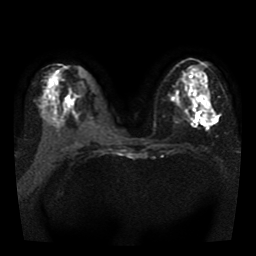
Breast MRI, one axial slice. Slice 17 of 41 in the series (ordered by position). Diffusion-weighted series; image 2 of 4 stored at this slice position (different b-values; order by instance number). 1.5 T. 256 × 256 image matrix, field of view 330 × 330 mm. Female patient.
Outlined on this slice (expert manual segmentation):
- tumour on diffusion-weighted imaging: bounding box [x1, y1, x2, y2] px = [204, 105, 216, 124]